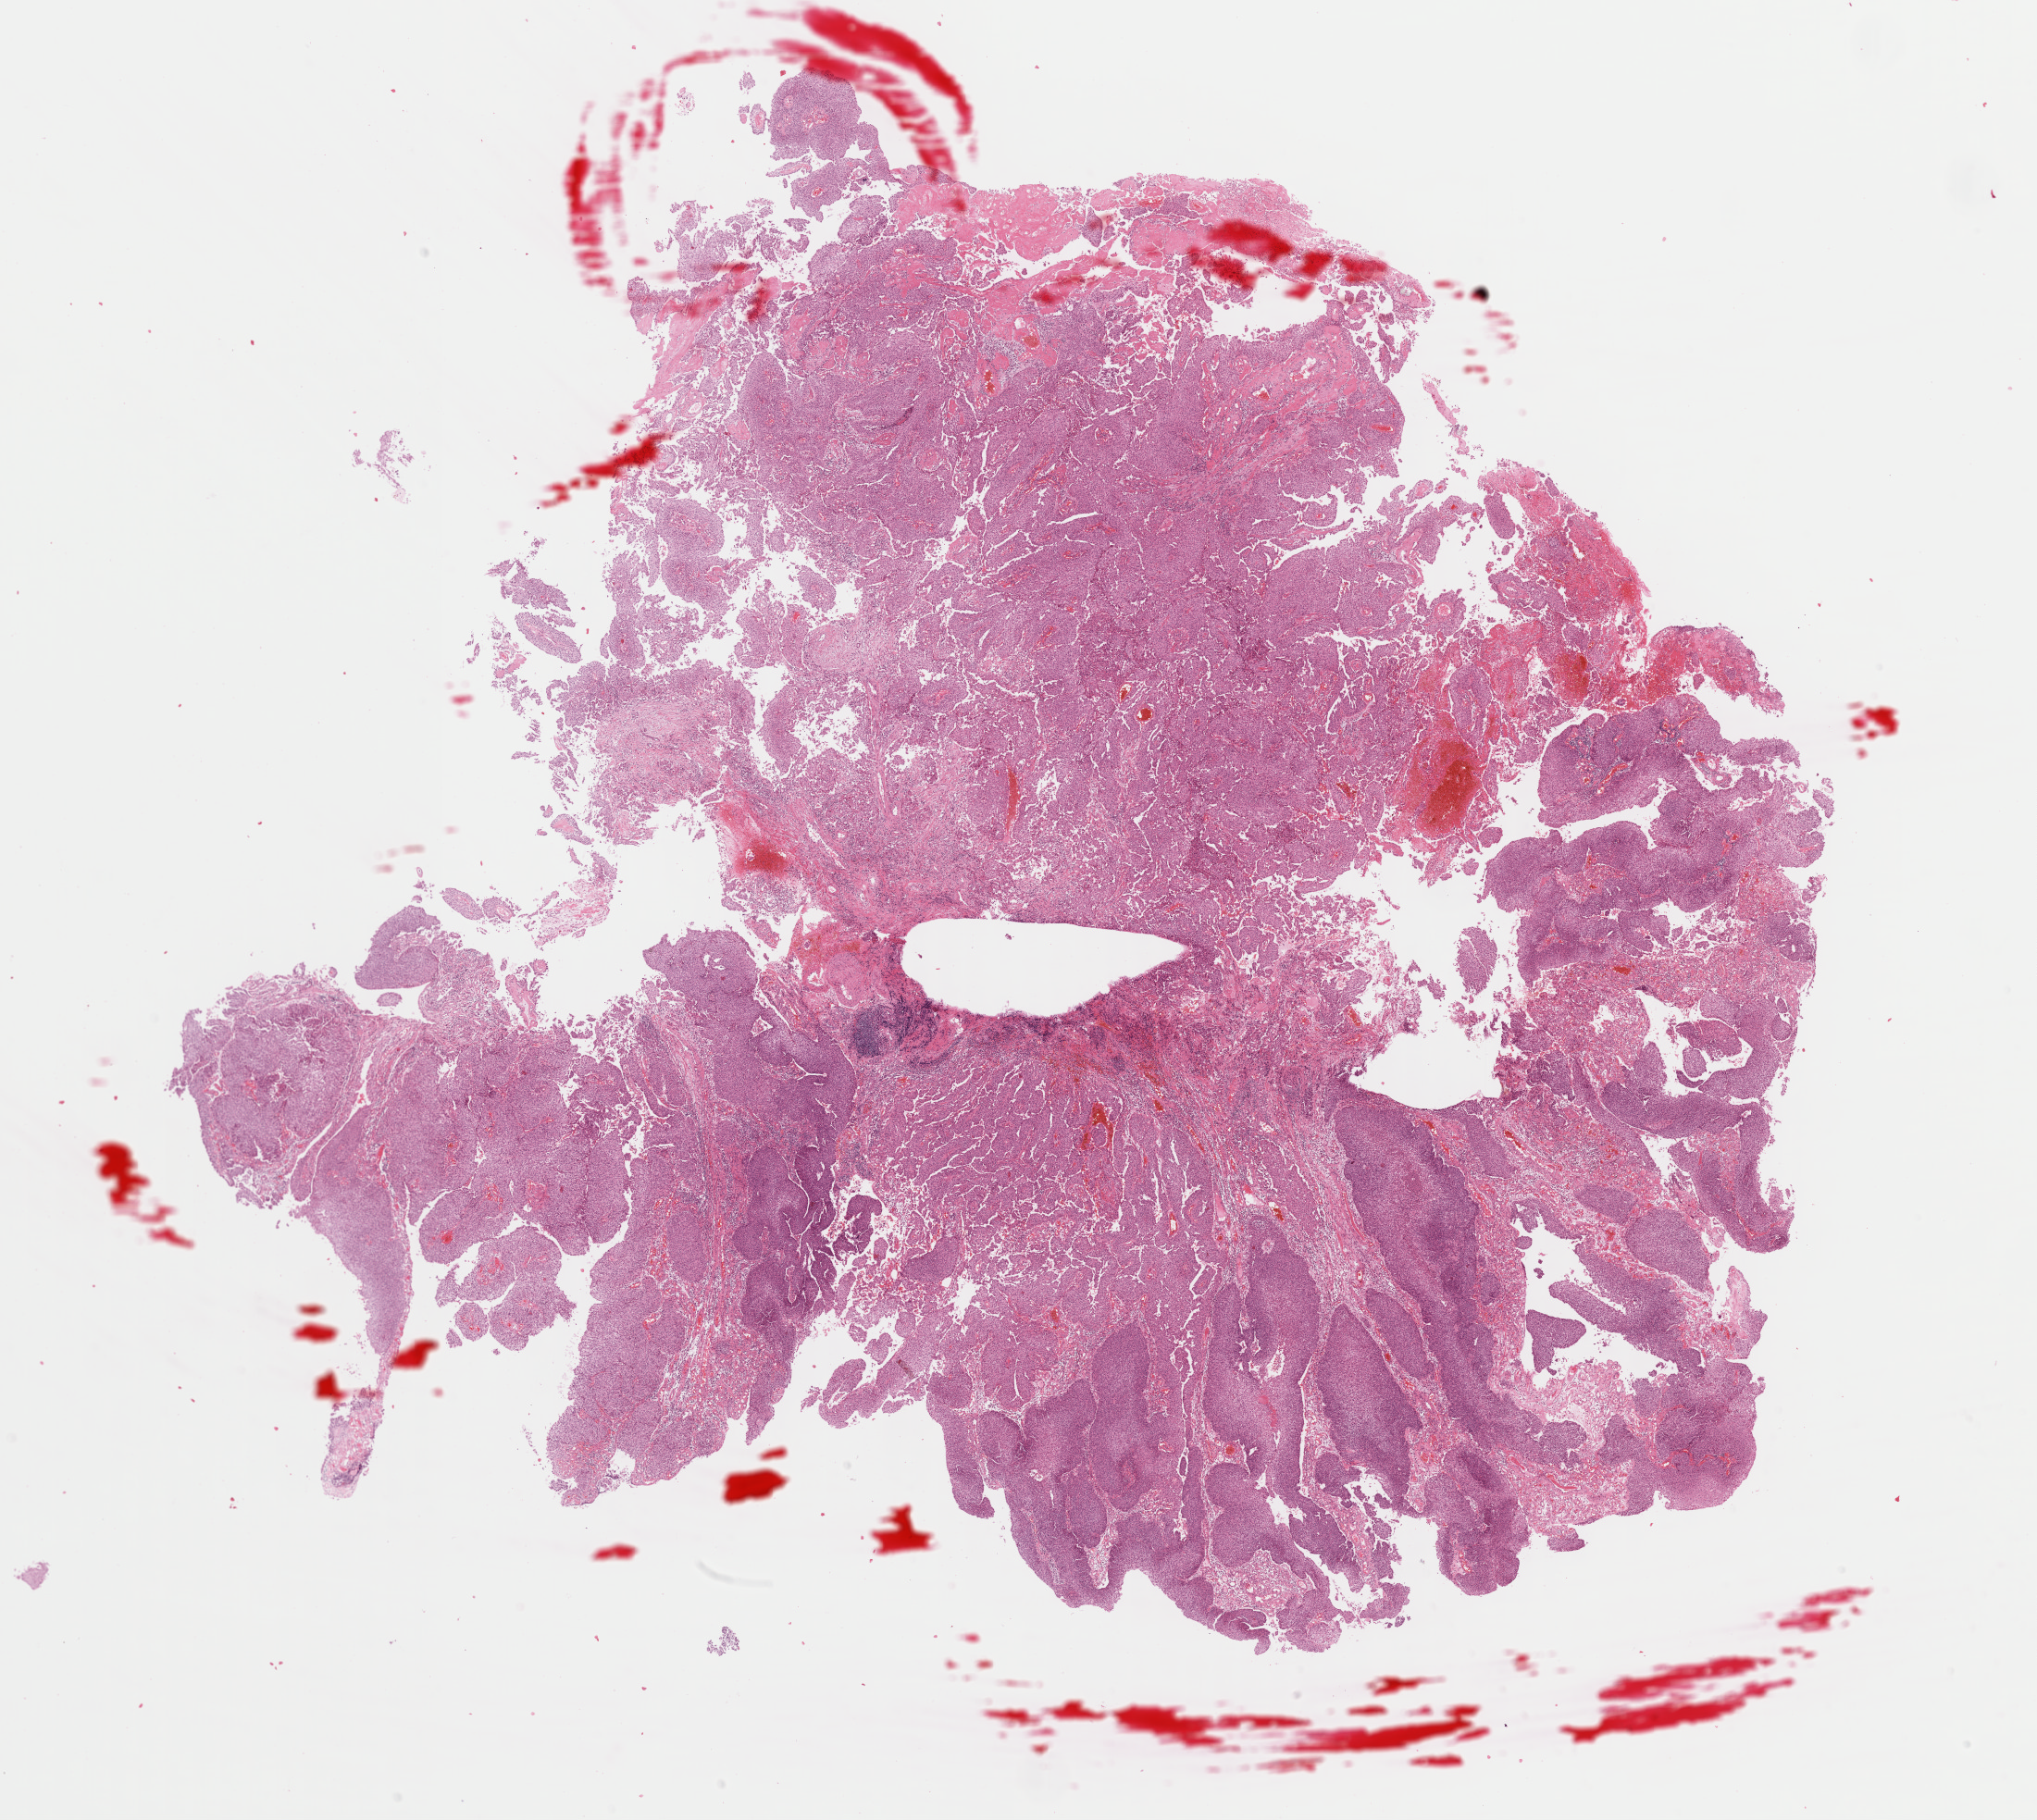
H&E-stained whole-slide image — shown as a low-resolution overview of the whole scanned area (about 17.4 x 15.5 mm, slide scanned at 40x), formalin-fixed paraffin-embedded (FFPE) diagnostic section, primary tumour sample from the bladder. Patient: male, age at initial diagnosis 70 years.
Histologic diagnosis: Transitional cell carcinoma (lateral wall of bladder).